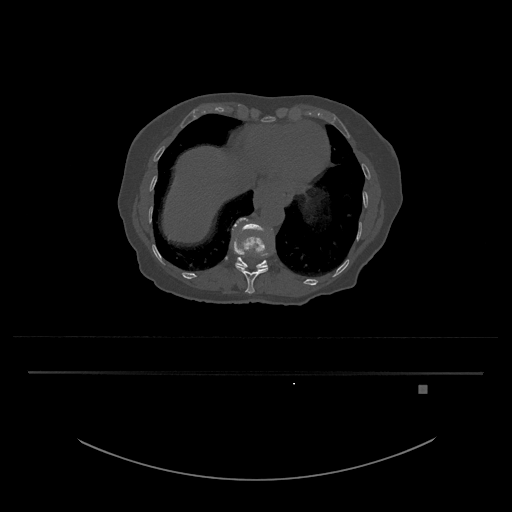
CT including the spine, one axial slice. Reconstruction kernel Br40s/3. 120 kVp. Bone window (W 1800 / L 400 HU). 0.5 mm slice thickness. 512 × 512 image matrix, field of view 500 × 500 mm. Female patient, age 57 years. From the clinical record (not read from this slice): primary cancer: cervical.
Outlined on this slice (semi-automatically segmented with operator editing):
- T11 vertebra: bounding box [x1, y1, x2, y2] px = [235, 264, 268, 294]
- T12 vertebra: [232, 217, 270, 269]